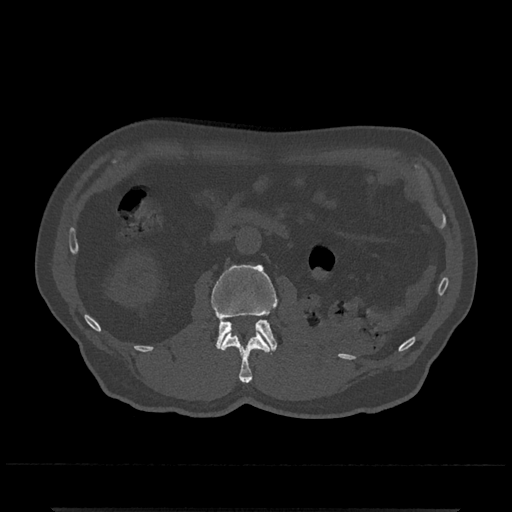
CT including the spine, one axial slice. Slice 318 of 797 in the series (ordered by position). Reconstruction kernel Br40s/3. Bone window (W 1800 / L 400 HU). 0.5 mm slice thickness. 512 × 512 image matrix, field of view 393 × 393 mm. Male patient, age 67 years. From the clinical record (not read from this slice): primary cancer: prostate.
Structures marked on this image (semi-automatically segmented with operator editing):
- L1 vertebra: box from (x=221, y=331) to (x=270, y=383) px
- L2 vertebra: (x=211, y=264)–(x=278, y=354)